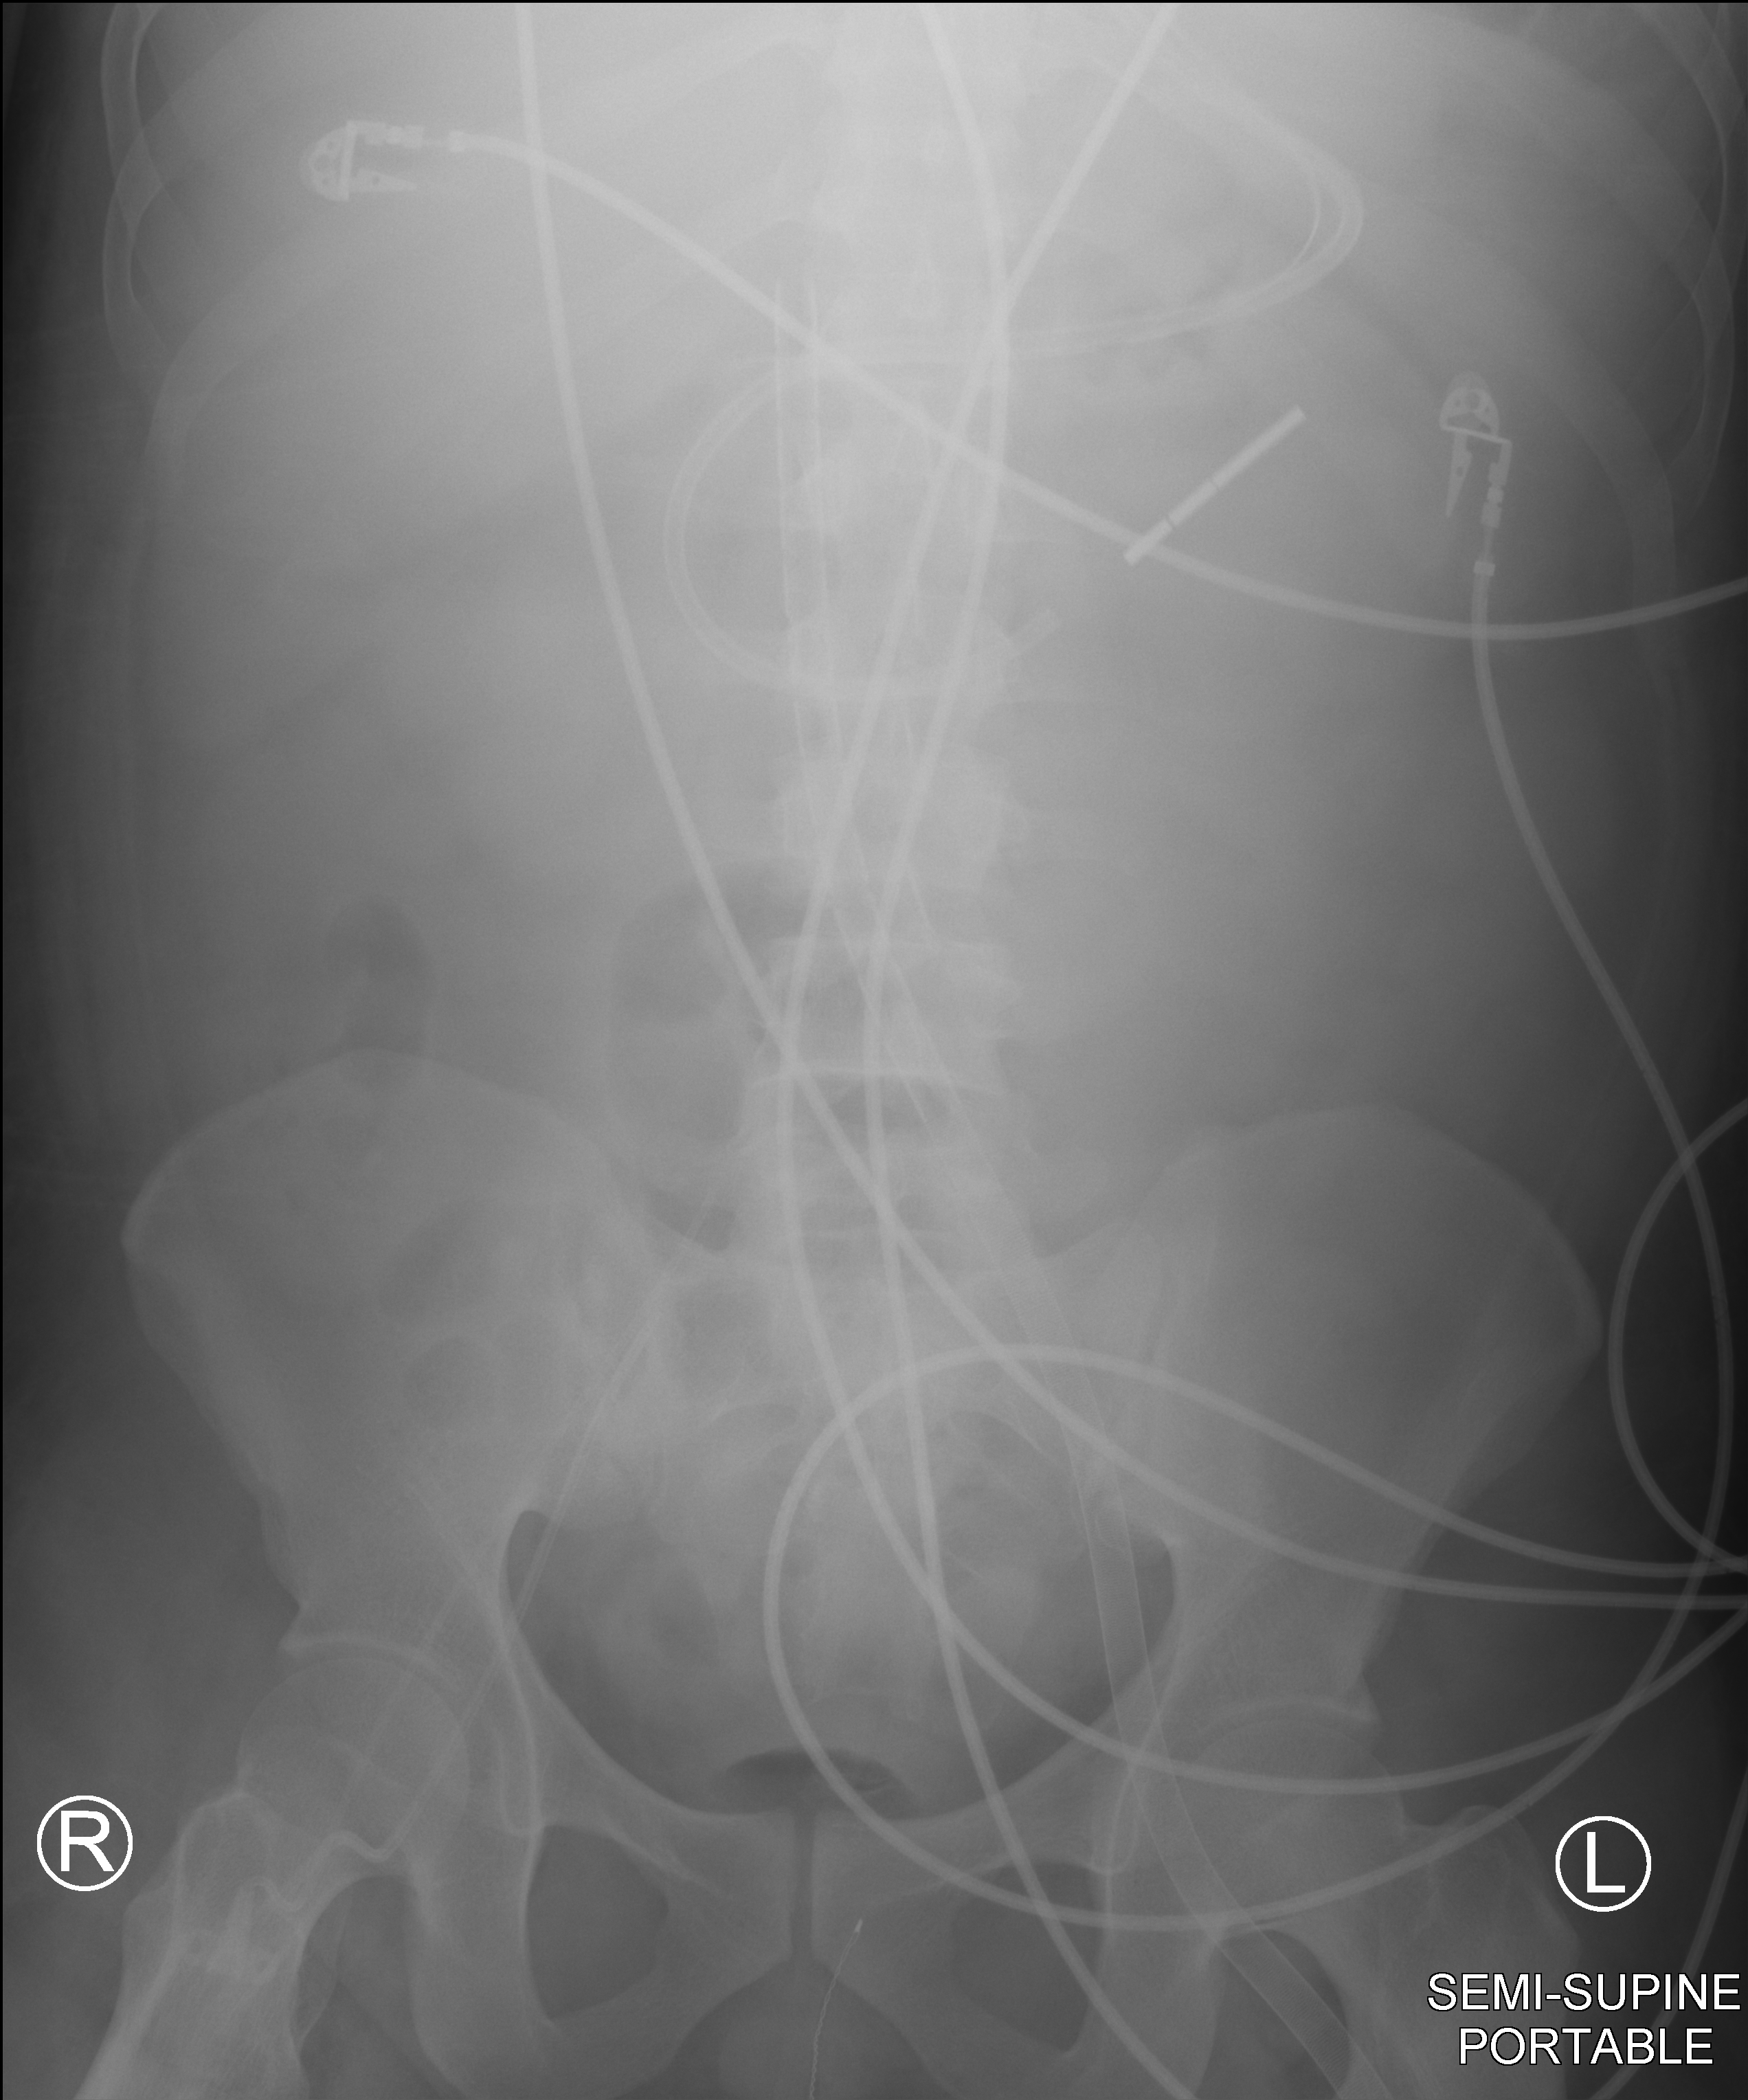
Bedside abdomen radiograph (computed radiography), anteroposterior (AP) projection. Patient hospitalised with COVID-19, aged 18–59 years.
Hospital-stay facts (about this admission, not read from this image; timing relative to this image not recorded):
- mechanically ventilated during this hospital stay: yes
- admitted to intensive care during this hospital stay: yes
- length of hospital stay: 60 days